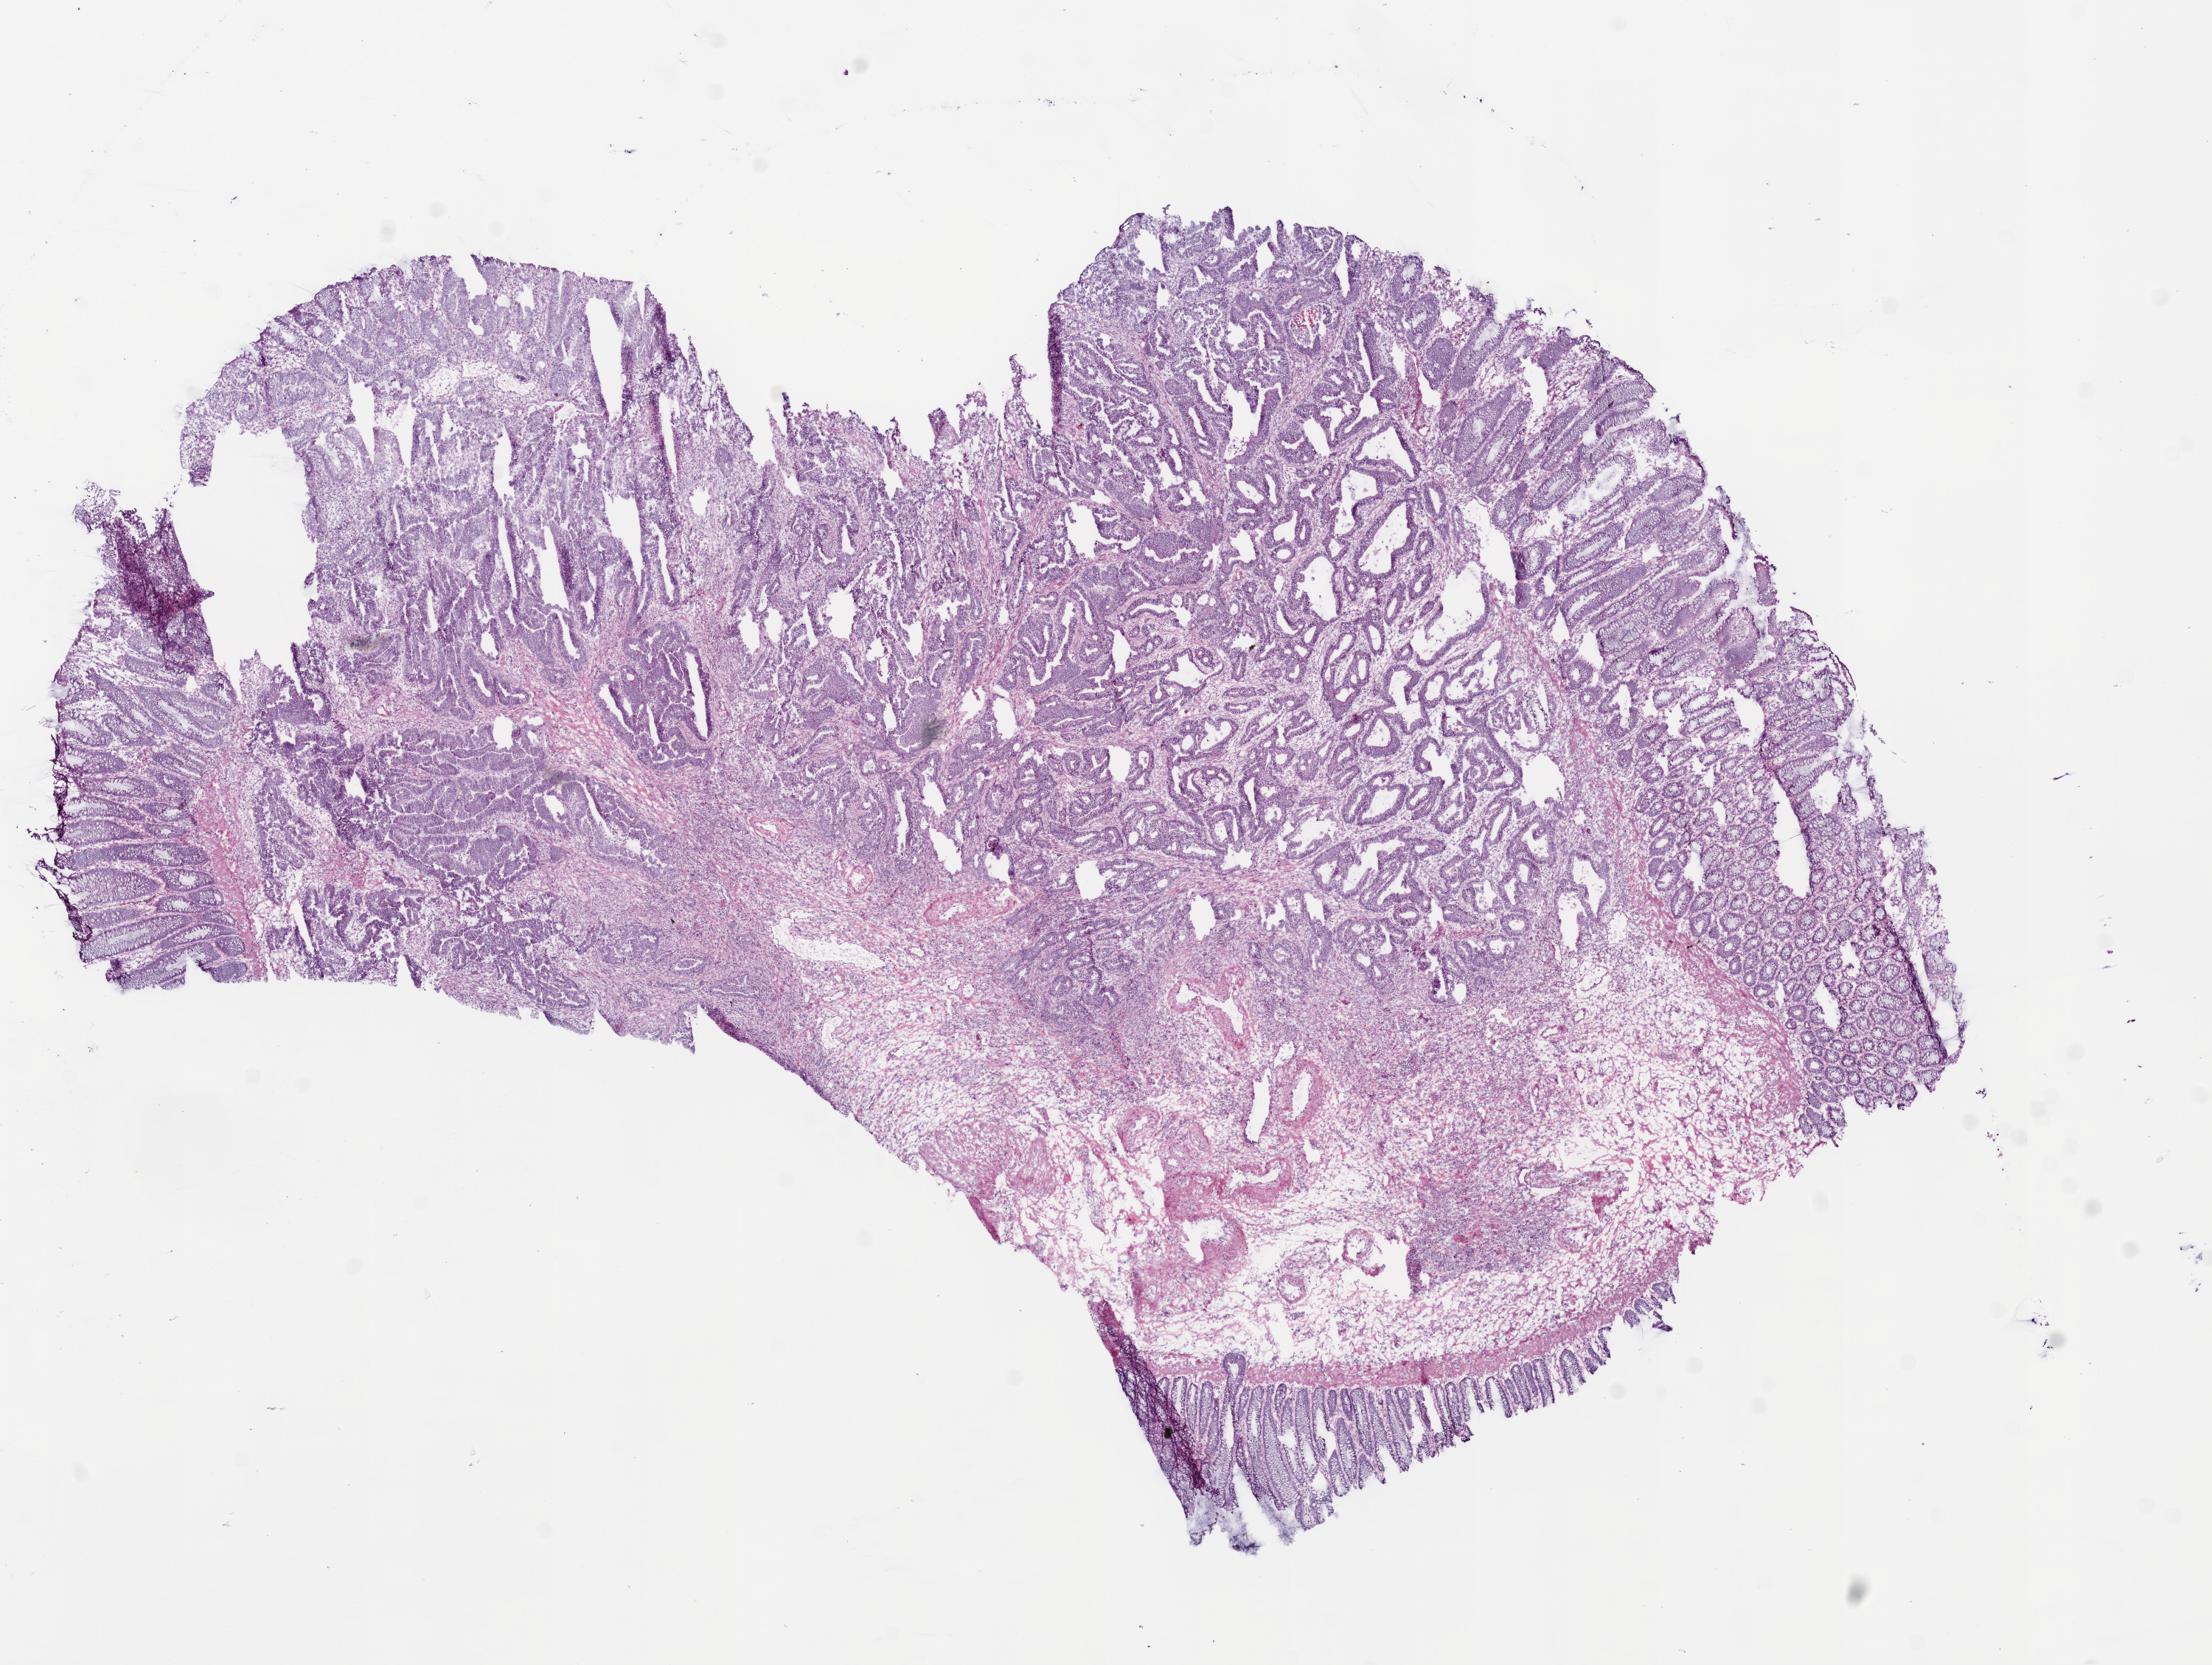
Whole-slide histology image, Hematoxylin and eosin (H&E) stained, low-resolution overview of the scanned area, about 12.0 x 9.1 mm. Frozen section from the bottom of the tissue portion. Sample: primary tumour, rectum. Male, age 74 years at initial diagnosis. Slide review estimates, as recorded: tumour cells 65%, tumour nuclei 70%, normal cells 10%, stromal cells 20%, necrosis 5%.
AJCC pathologic stage: IIIB. Lymph nodes positive (case pathology): 1 of 14 examined. Histologic diagnosis: Adenocarcinoma, NOS.